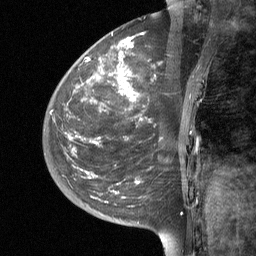
Breast MRI (dynamic contrast-enhanced), one sagittal slice; position 14 of 64 along the scan axis; dynamic contrast-enhanced study with each time point stored as its own series, time point 2 of 3 at this slice position (early post-contrast, ordered by acquisition time); 1.5 T; TE 4.8 ms, TR 27 ms; 256 × 256 image matrix. Female patient, age 42 years. From the clinical record (not read from this slice): setting: breast cancer imaged before/during neoadjuvant chemotherapy; receptor status: triple-negative.
Outlined on this slice (semi-automatic segmentation, software-assisted and operator-edited):
- analysis volume of interest (the breast-tissue region the enhancement analysis was run in; not a lesion): box from (x=43, y=29) to (x=203, y=190) px
- tumour enhancement mask (voxels above the 90 % enhancement threshold inside the analysis volume of interest): (x=85, y=32)–(x=162, y=184)